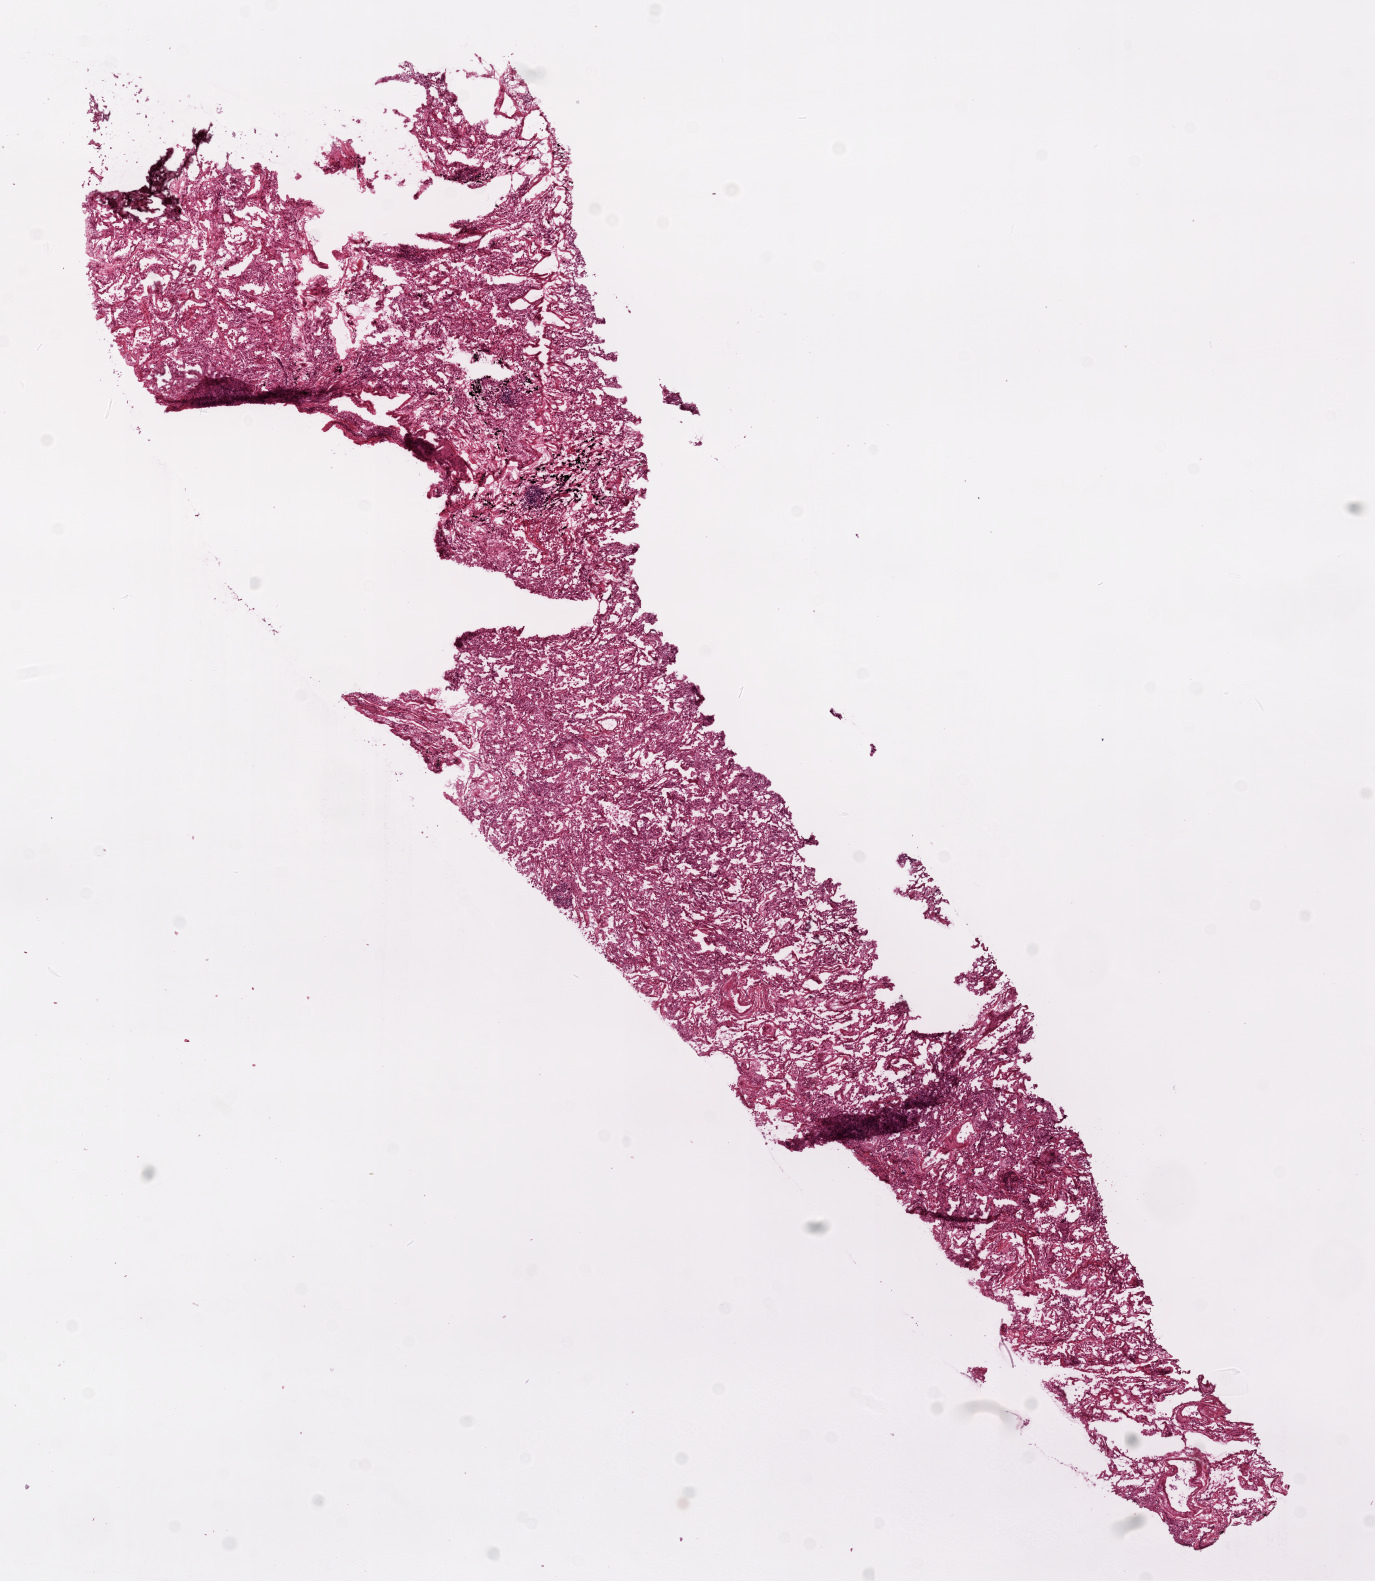
Whole-slide histology image, H&E — a low-resolution overview of the entire scanned area, about 11.0 x 12.7 mm (from a 20x scan), frozen section from the top of the tissue portion, lung, solid tissue normal (non-tumour tissue) sample. Female patient; age at initial diagnosis 76 years.
This section: solid tissue normal (non-tumour) sample from the same patient. Patient diagnosis: Squamous cell carcinoma, NOS (lower lobe, lung).